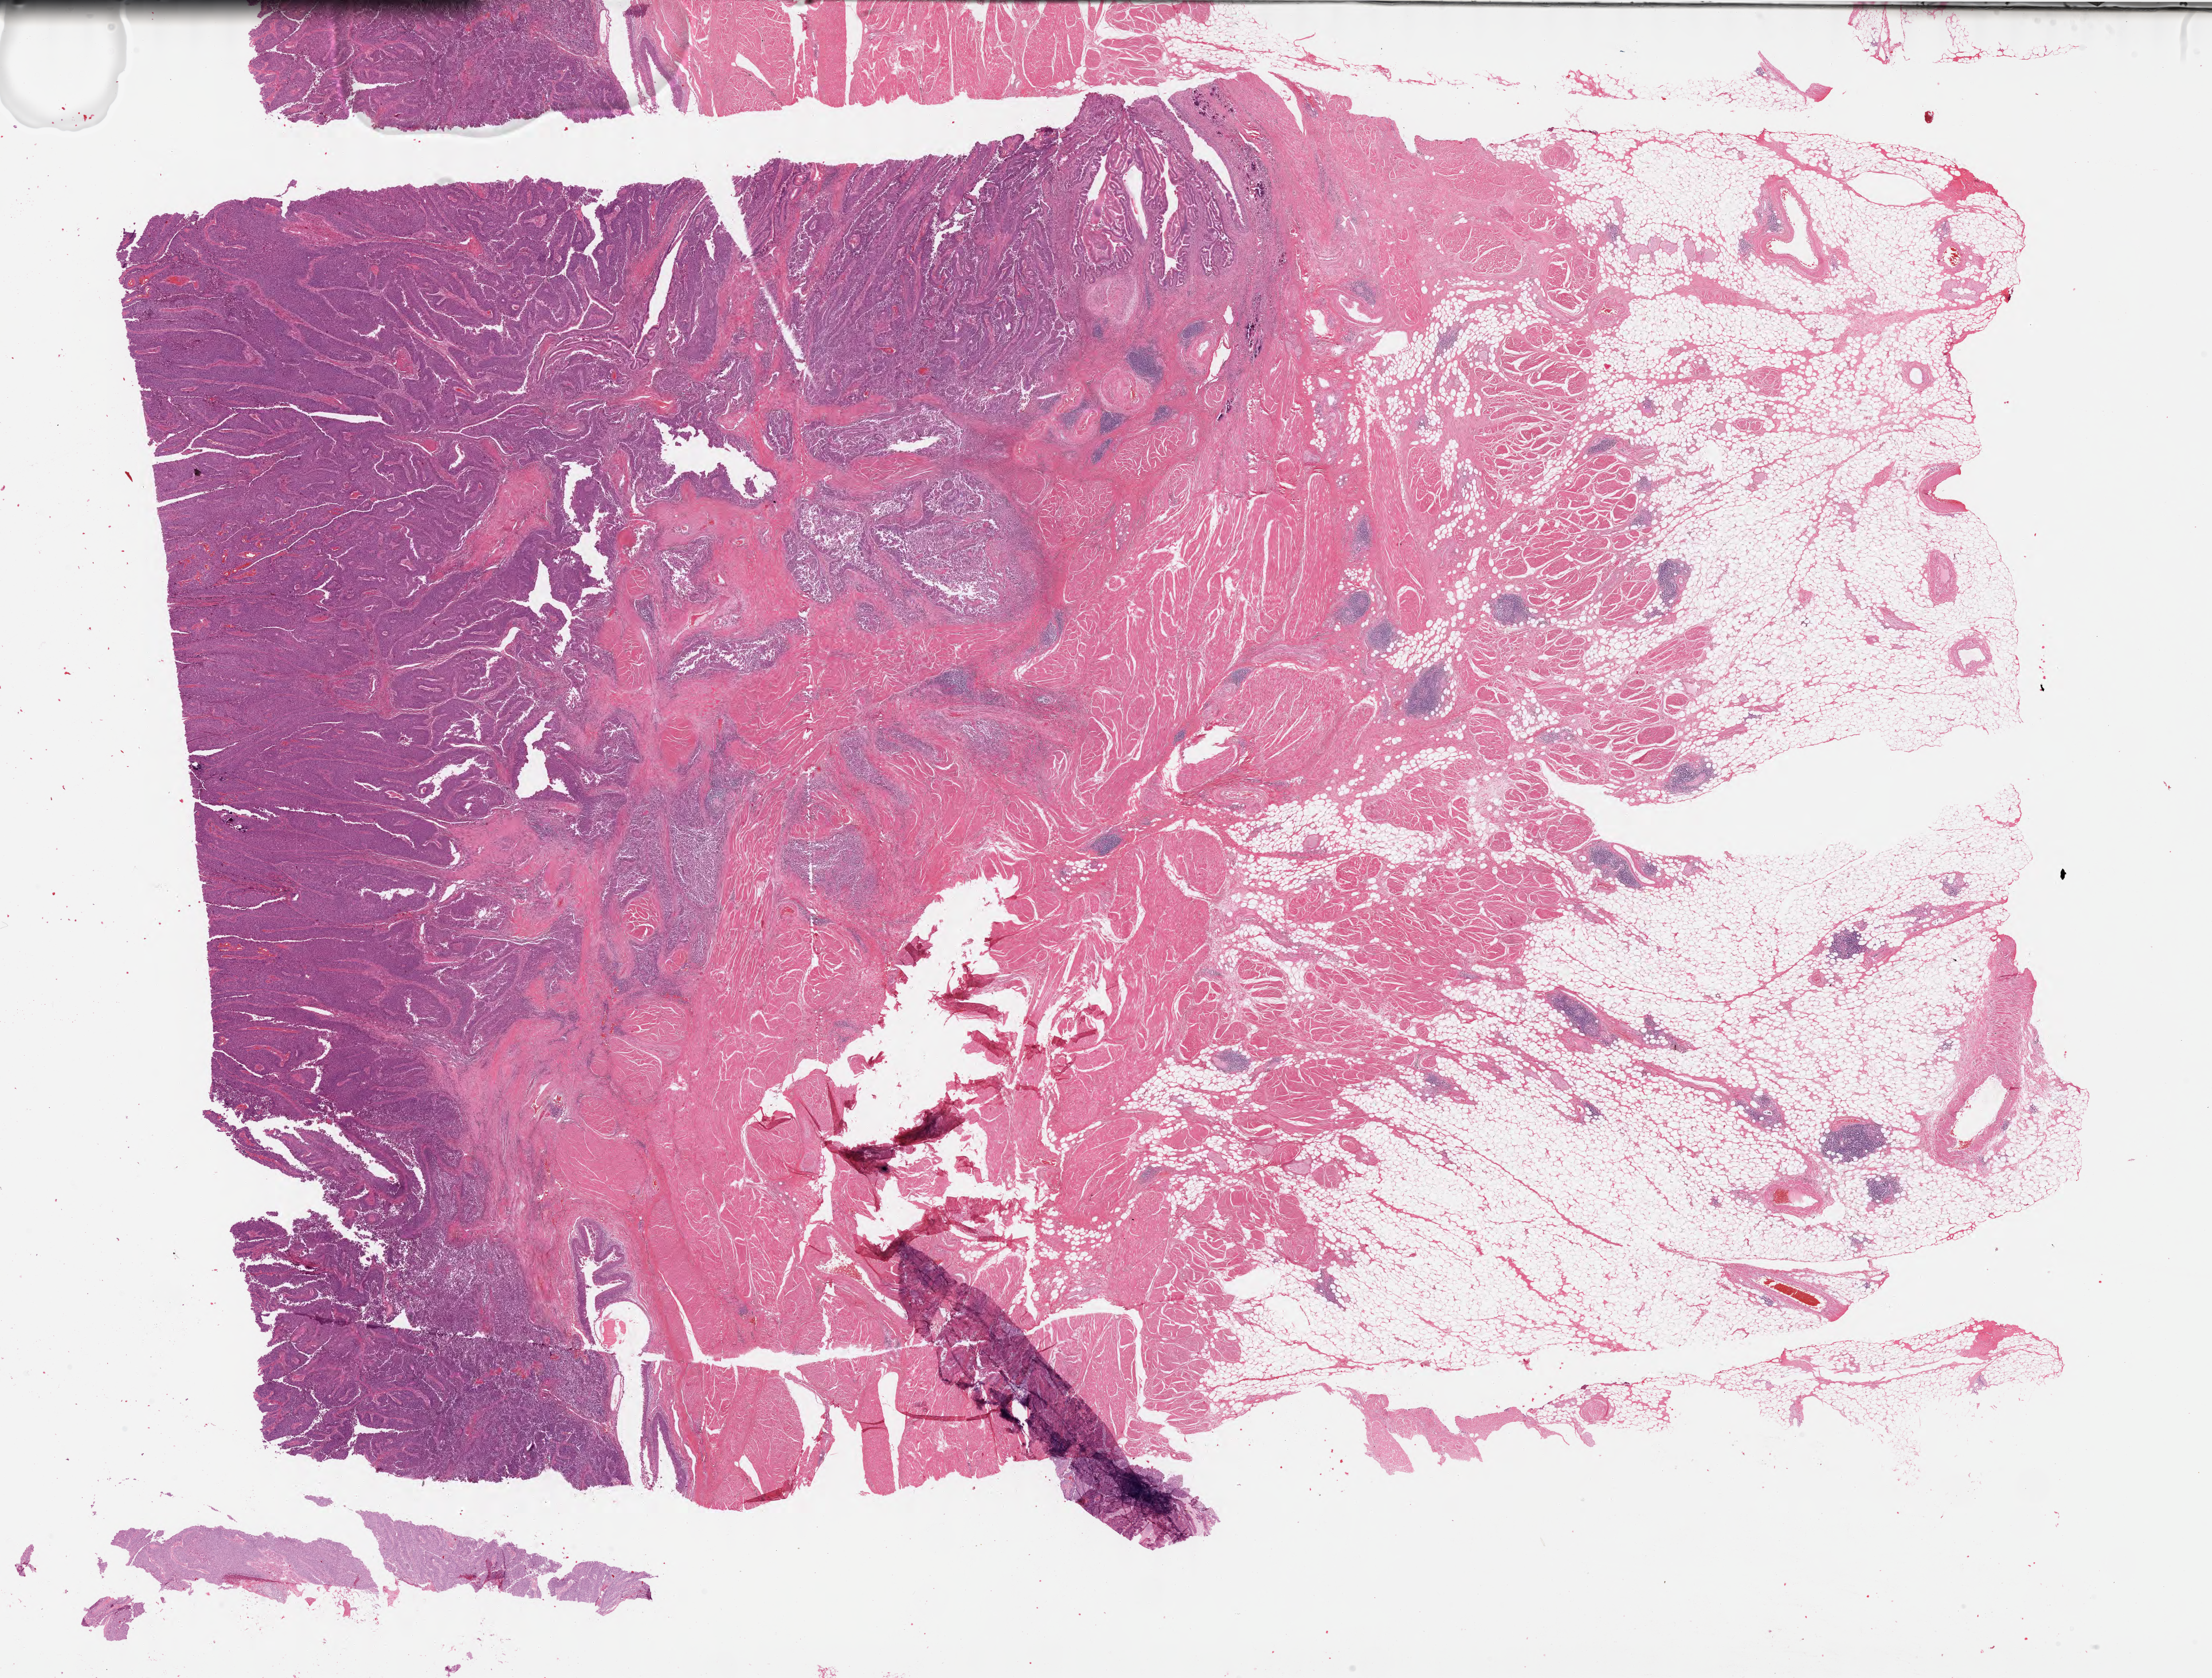
H&E-stained whole-slide image — low-resolution overview of the scanned area, about 30.4 x 23.1 mm, FFPE section, bladder, primary tumour sample. Male, age 54 years at initial diagnosis.
Diagnosis: Papillary transitional cell carcinoma.